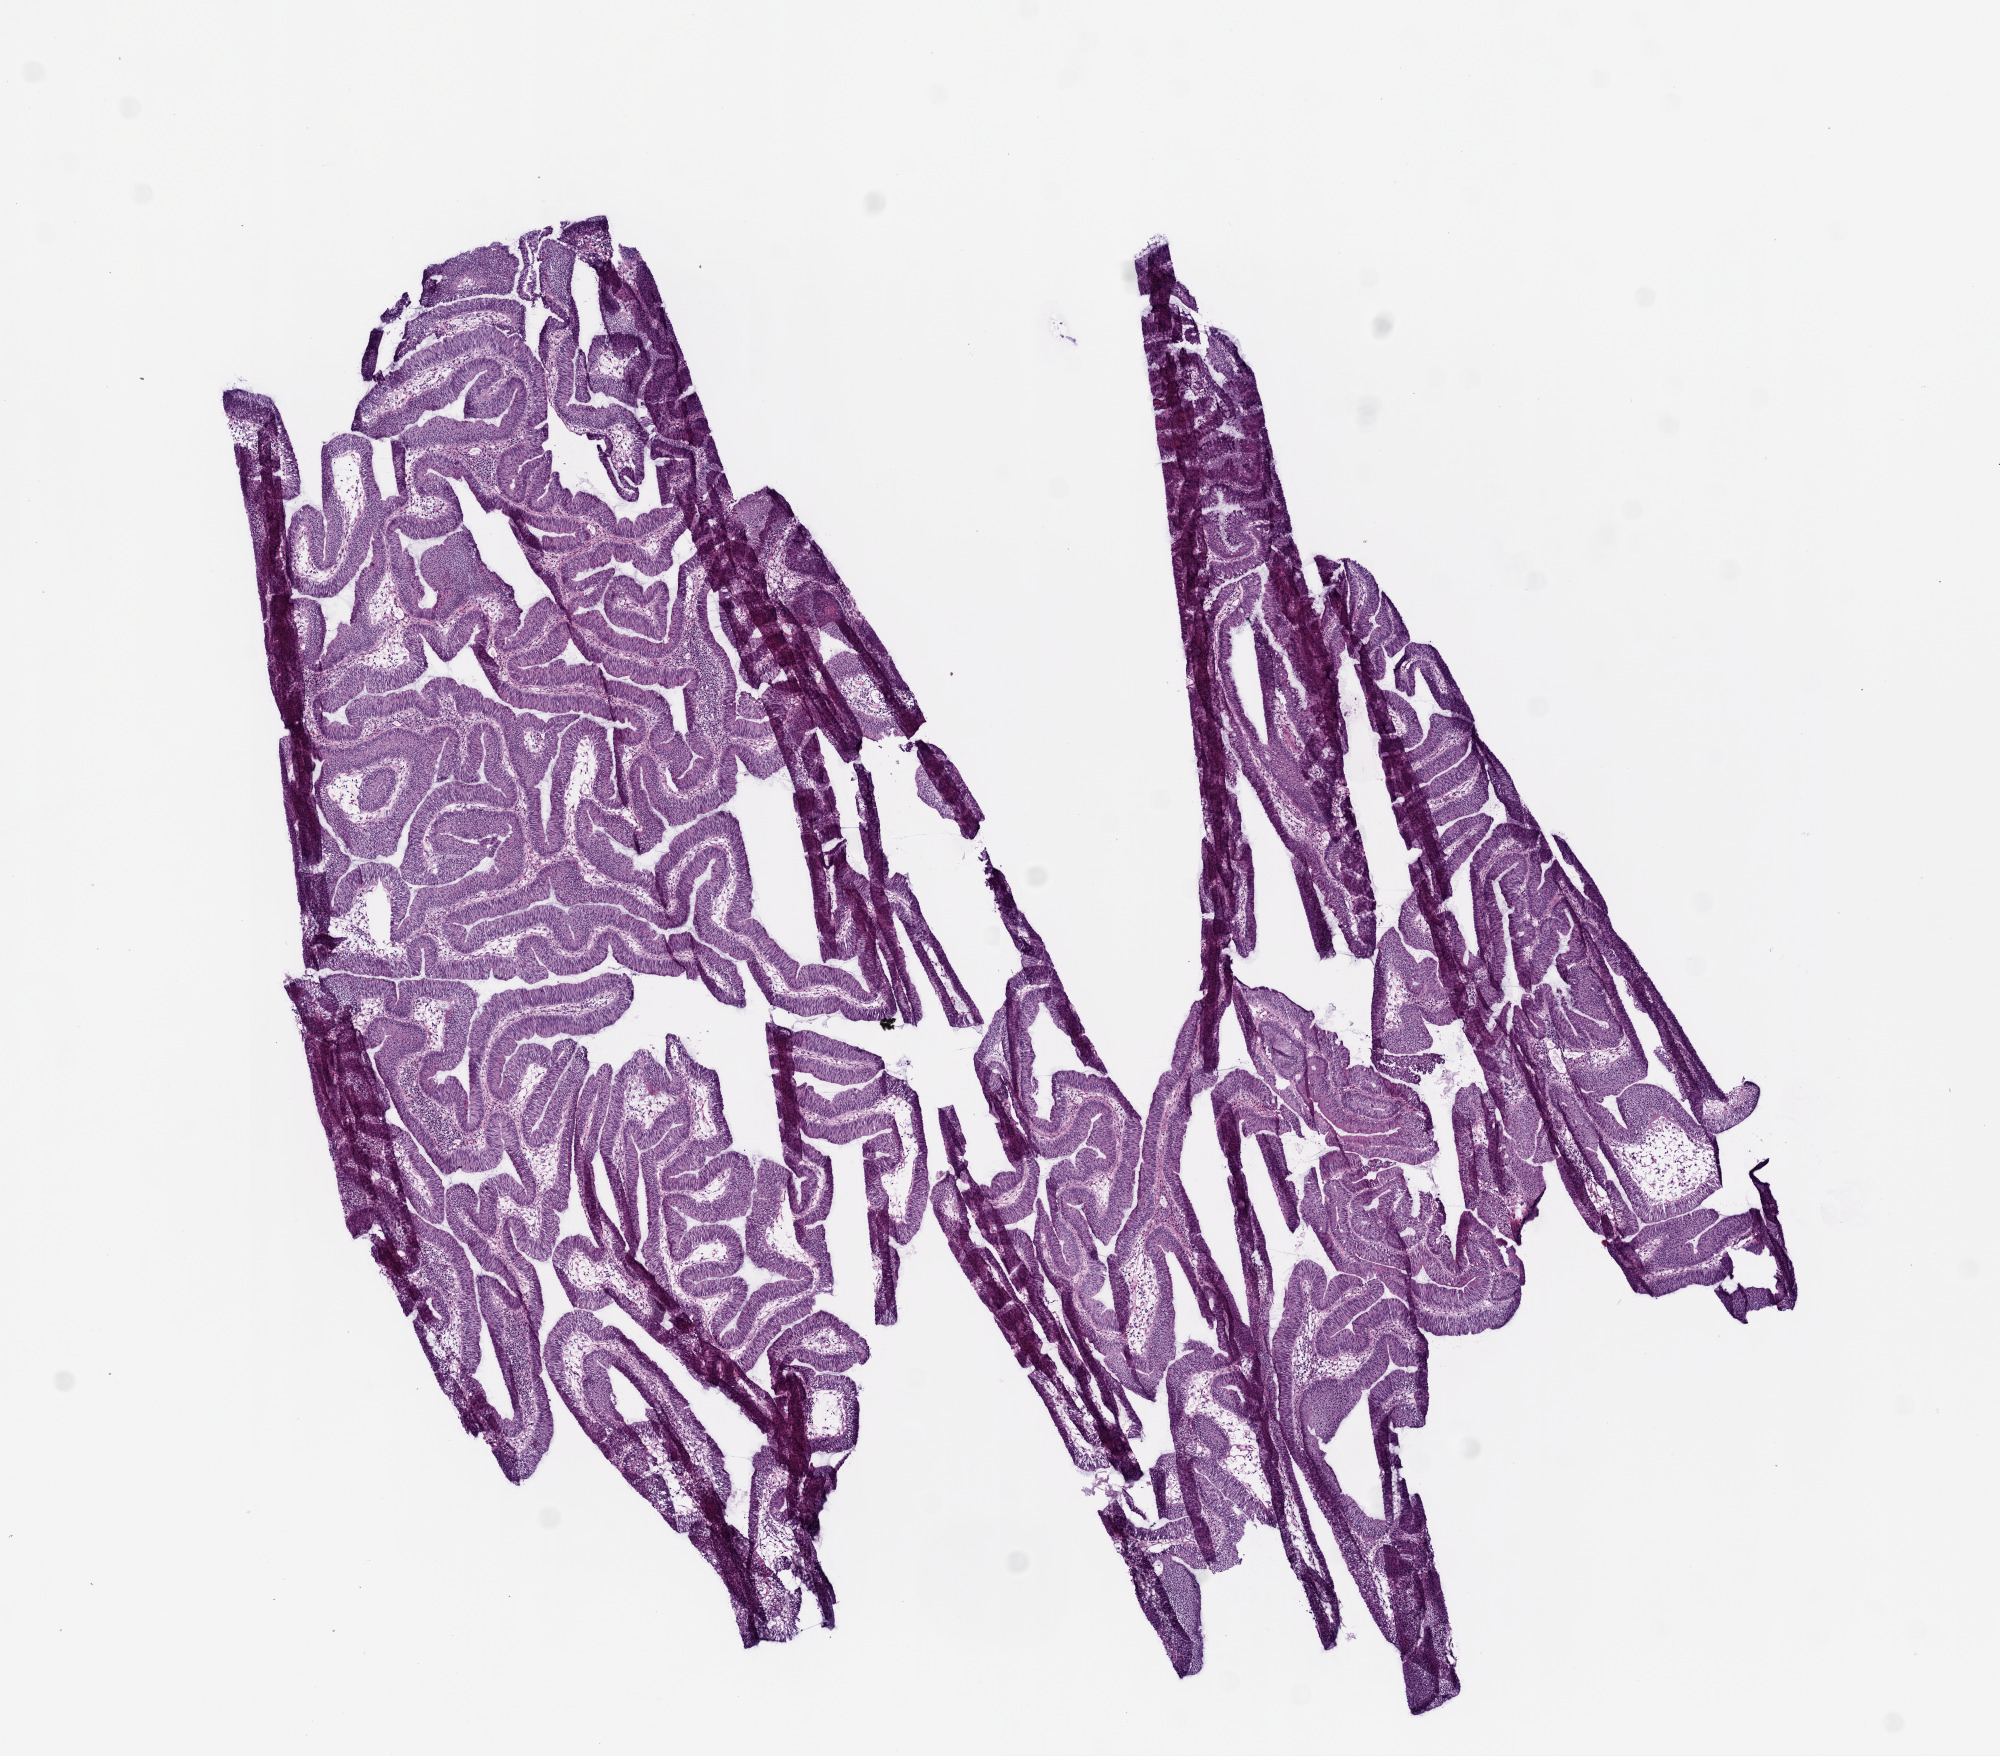
Whole-slide histology image, H&E-stained — whole scanned area (about 8.0 x 7.0 mm) shown as a low-resolution overview, frozen section from the top of the tissue portion, primary tumour sample from the colon. Patient: male, age at initial diagnosis 73 years. Slide review estimates, as recorded: tumour cells 90%, tumour nuclei 80%, normal cells 0%, stromal cells 10%, necrosis 0%.
• AJCC pathologic stage: I (5th edition)
• diagnosis: Adenocarcinoma, NOS
• TNM: T2 N0 M0